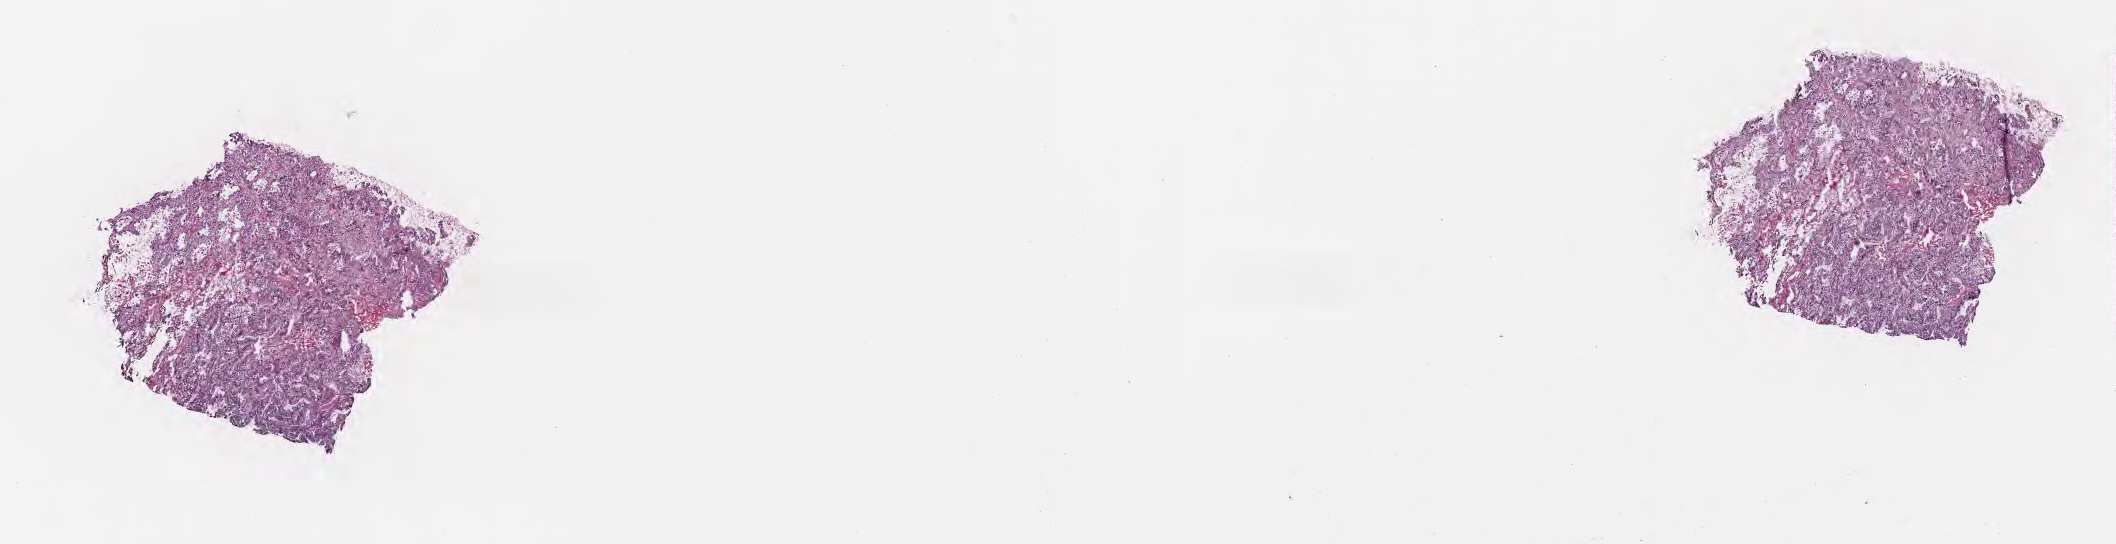
Whole-slide image, H&E stain — whole scanned area (about 17.1 x 4.4 mm) shown as a low-resolution overview; frozen section (tissue freezing medium); primary tumor; anatomic site: upper lobe of right lung. Male patient, aged 62. Slide review estimates, as recorded: tumor cells 70%, tumor nuclei 80%, stromal cells 20%, necrosis 10%, normal cells 0%. Infiltration values recorded for this section: lymphocyte infiltration 3%, monocyte infiltration 3%, neutrophil infiltration 0%.
• diagnosis: Acinar cell carcinoma
• section: top of the tissue portion
• AJCC pathologic stage: Stage IIA